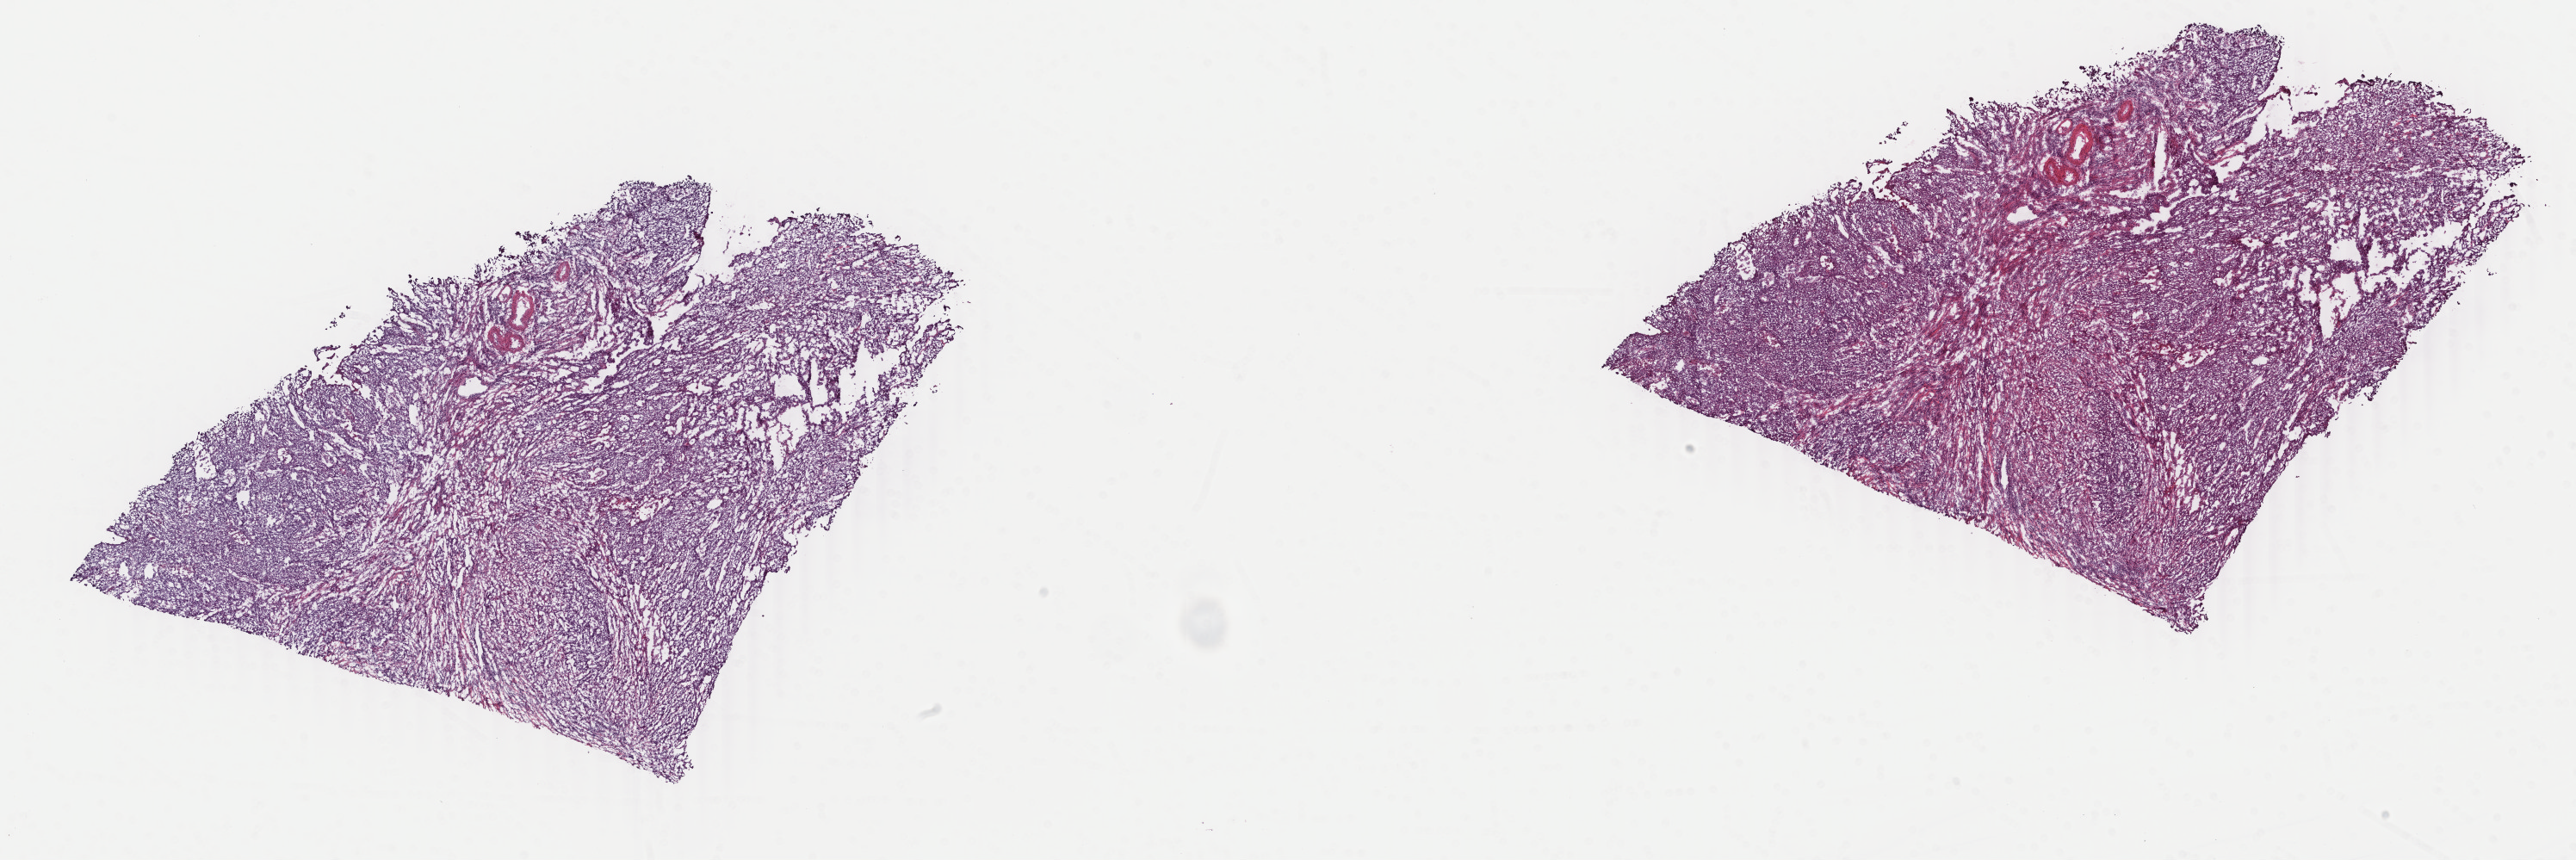
Whole-slide histology image, H&E — a low-resolution overview of the entire scanned area, about 23.8 x 7.9 mm (slide scanned at 40x); frozen section from the top of the tissue portion; cervix, primary tumour sample. Female patient; age at initial diagnosis 39 years. Slide review estimates, as recorded: tumour cells 85%, tumour nuclei 90%.
Histologic diagnosis: Squamous cell carcinoma, NOS (exocervix).